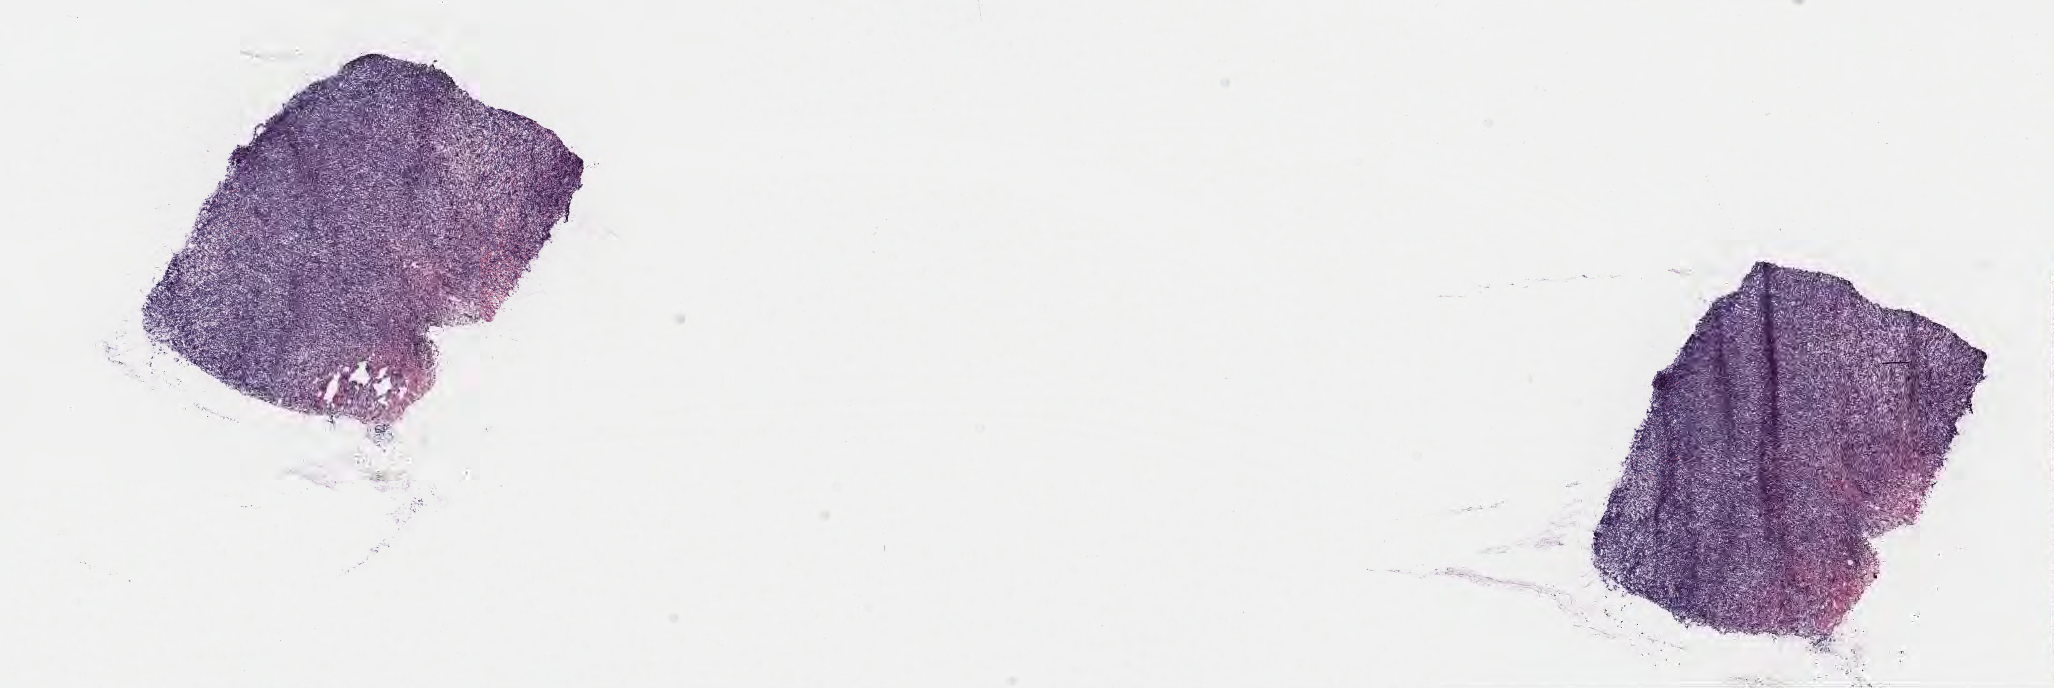
Haematoxylin and eosin whole-slide image — a low-resolution overview of the entire scanned area, about 16.6 x 5.6 mm; cryosection; specimen: primary tumor; site: cranium. Male patient, 46 years old. Pathologist review of this section (percent, as recorded): tumor cells 95%, tumor nuclei 95%, stromal cells 5%, necrosis 0%, normal cells 0%. Inflammatory infiltration, as recorded: lymphocyte infiltration 40%, monocyte infiltration 35%, neutrophil infiltration 5%.
- histologic diagnosis: Burkitt lymphoma, NOS
- Ann Arbor stage (patient): Stage IV
- section: top of the tissue portion